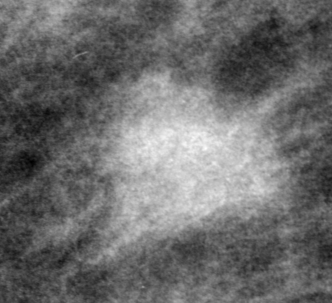
Crop from a digitized film mammogram around one marked abnormality, right breast, MLO view, BI-RADS breast density category 2 (scale 1–4).
Finding: mass, shape oval, margins obscured; BI-RADS assessment category 0; subtlety rating 5 on a 1 (subtle) to 5 (obvious) scale; pathology result (as recorded, not read from the image): malignant.